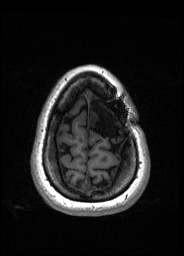
Pre-operative brain MRI before brain-tumour surgery, one axial slice; T1-weighted post-contrast; 1 mm slice thickness; 184 × 256 image matrix, field of view 180 × 250 mm. Case-level facts recorded for this patient, not image findings: histopathology: Oligodendroglioma; WHO grade: 2; IDH mutation: yes; tumour location: Left Frontal.
Annotated regions visible in this slice (outlined manually by an expert reader):
- tumour: bounding box (x1, y1, x2, y2) in pixels: (88, 111, 99, 127)